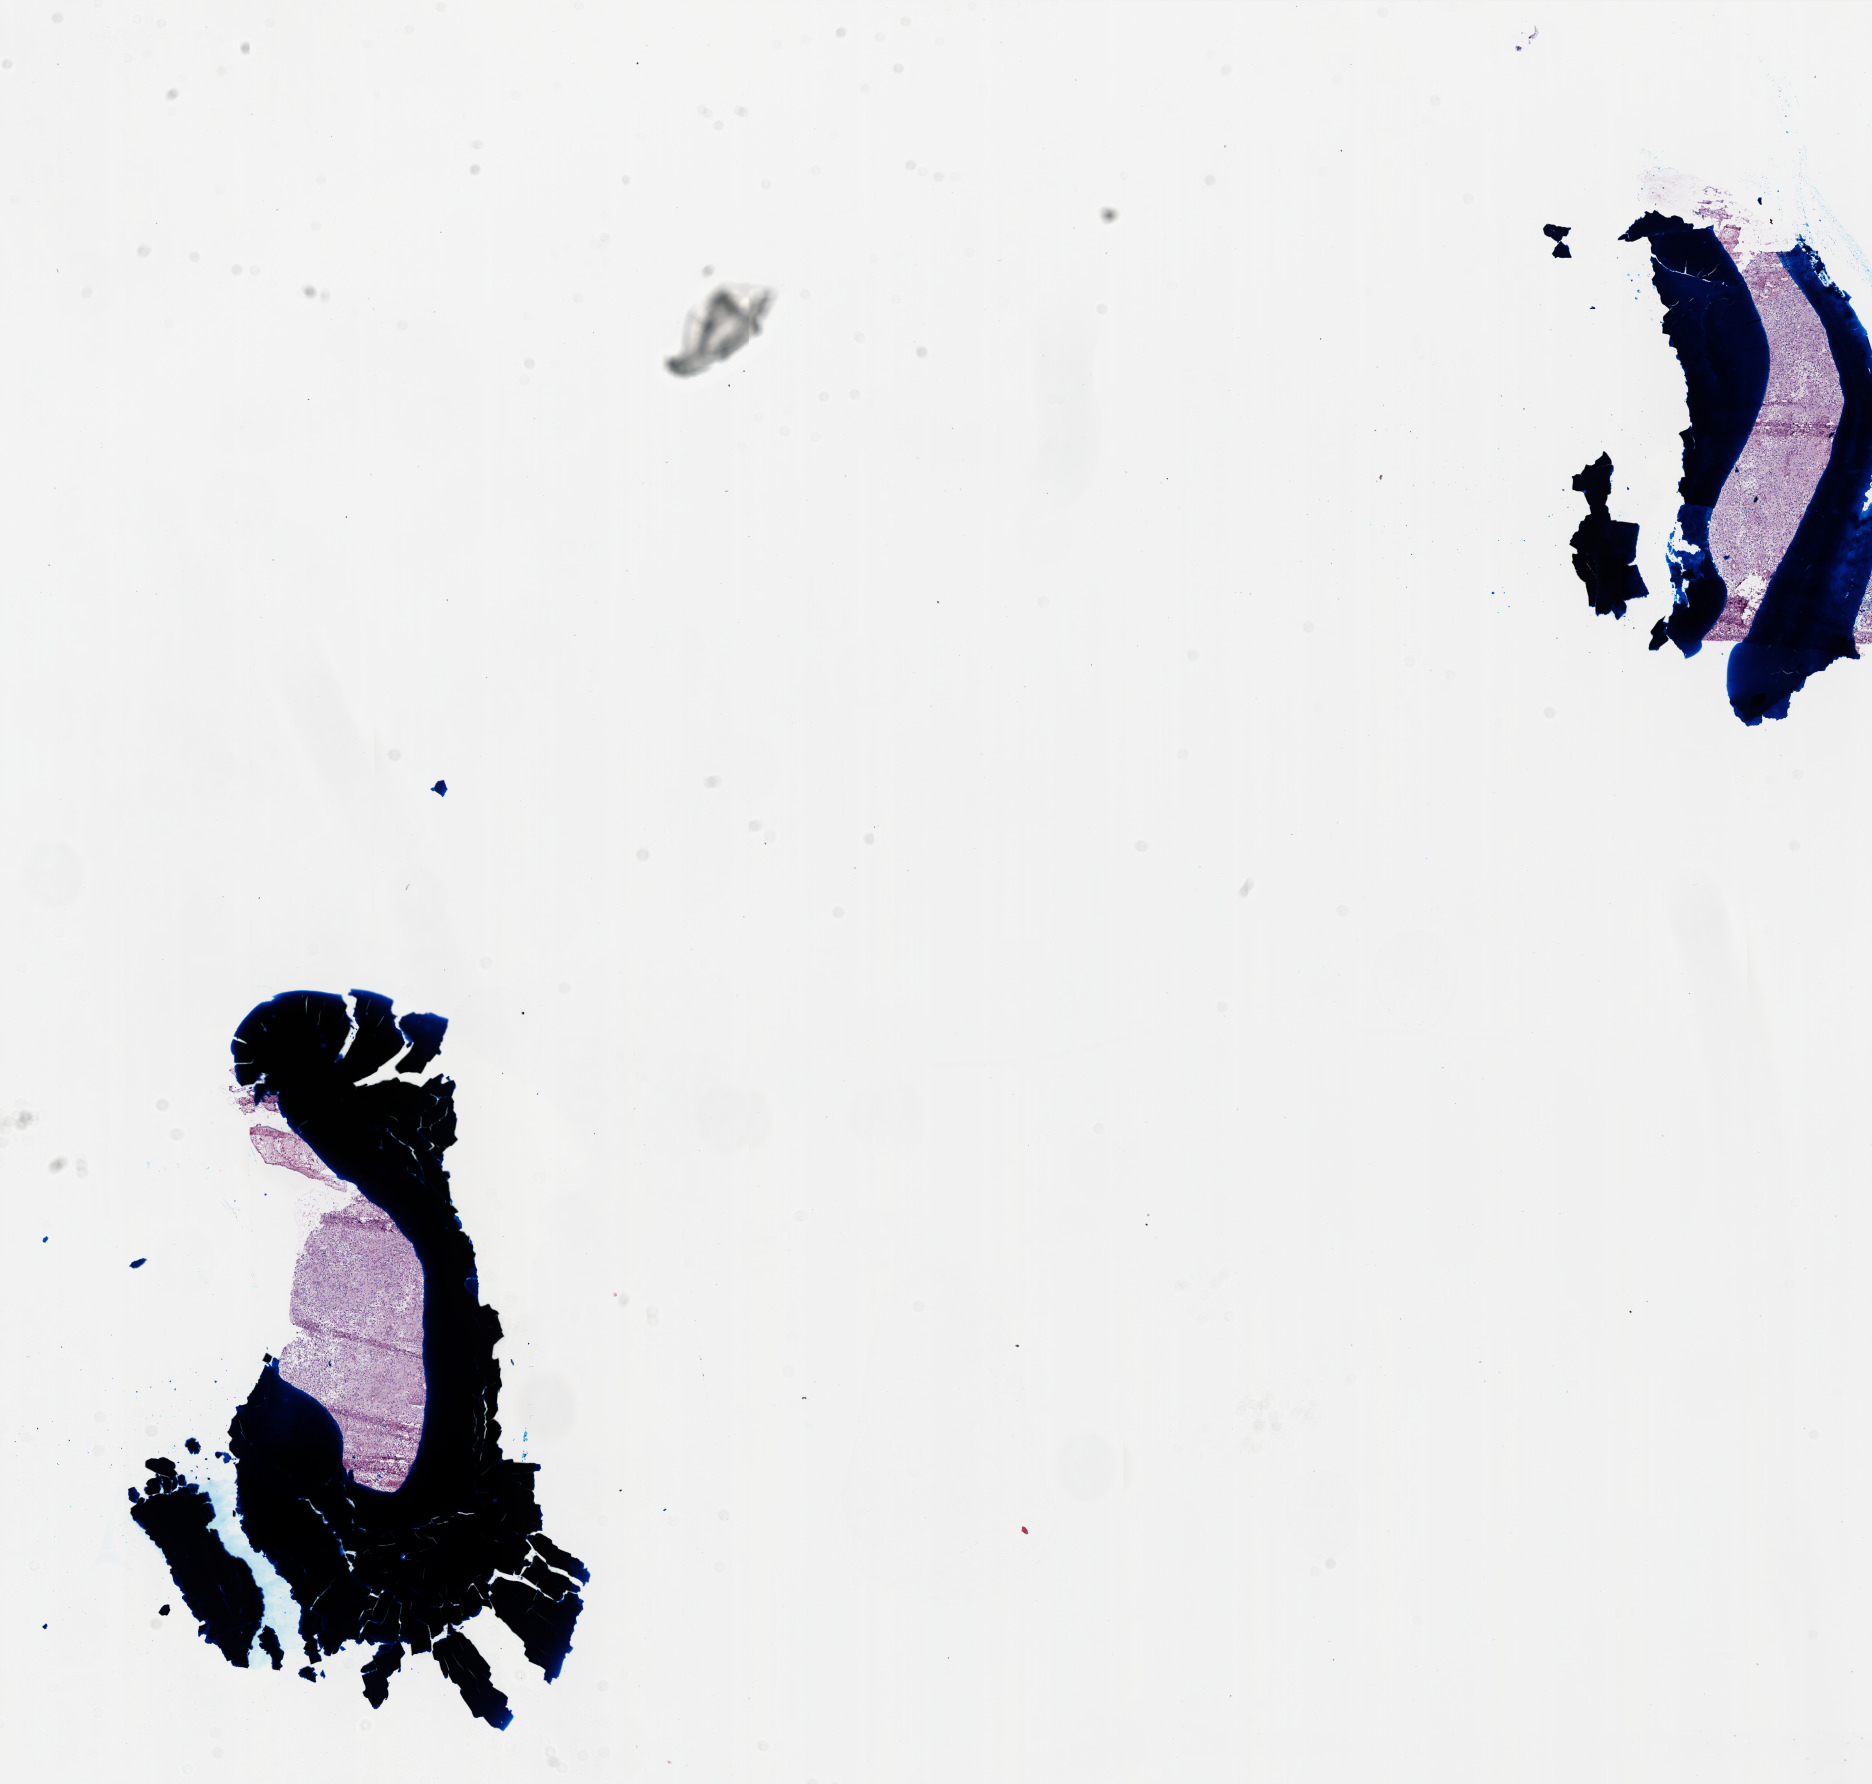
Digitized H&E-stained tissue section (whole slide) — a low-resolution overview of the entire scanned area, about 15.0 x 14.3 mm, frozen section from the top of the tissue portion, primary tumour sample from the brain. Patient: female, age at initial diagnosis 37 years. Pathologist review of this section (percent, as recorded): tumour cells 100%, tumour nuclei 95%.
Histologic diagnosis: Glioblastoma.